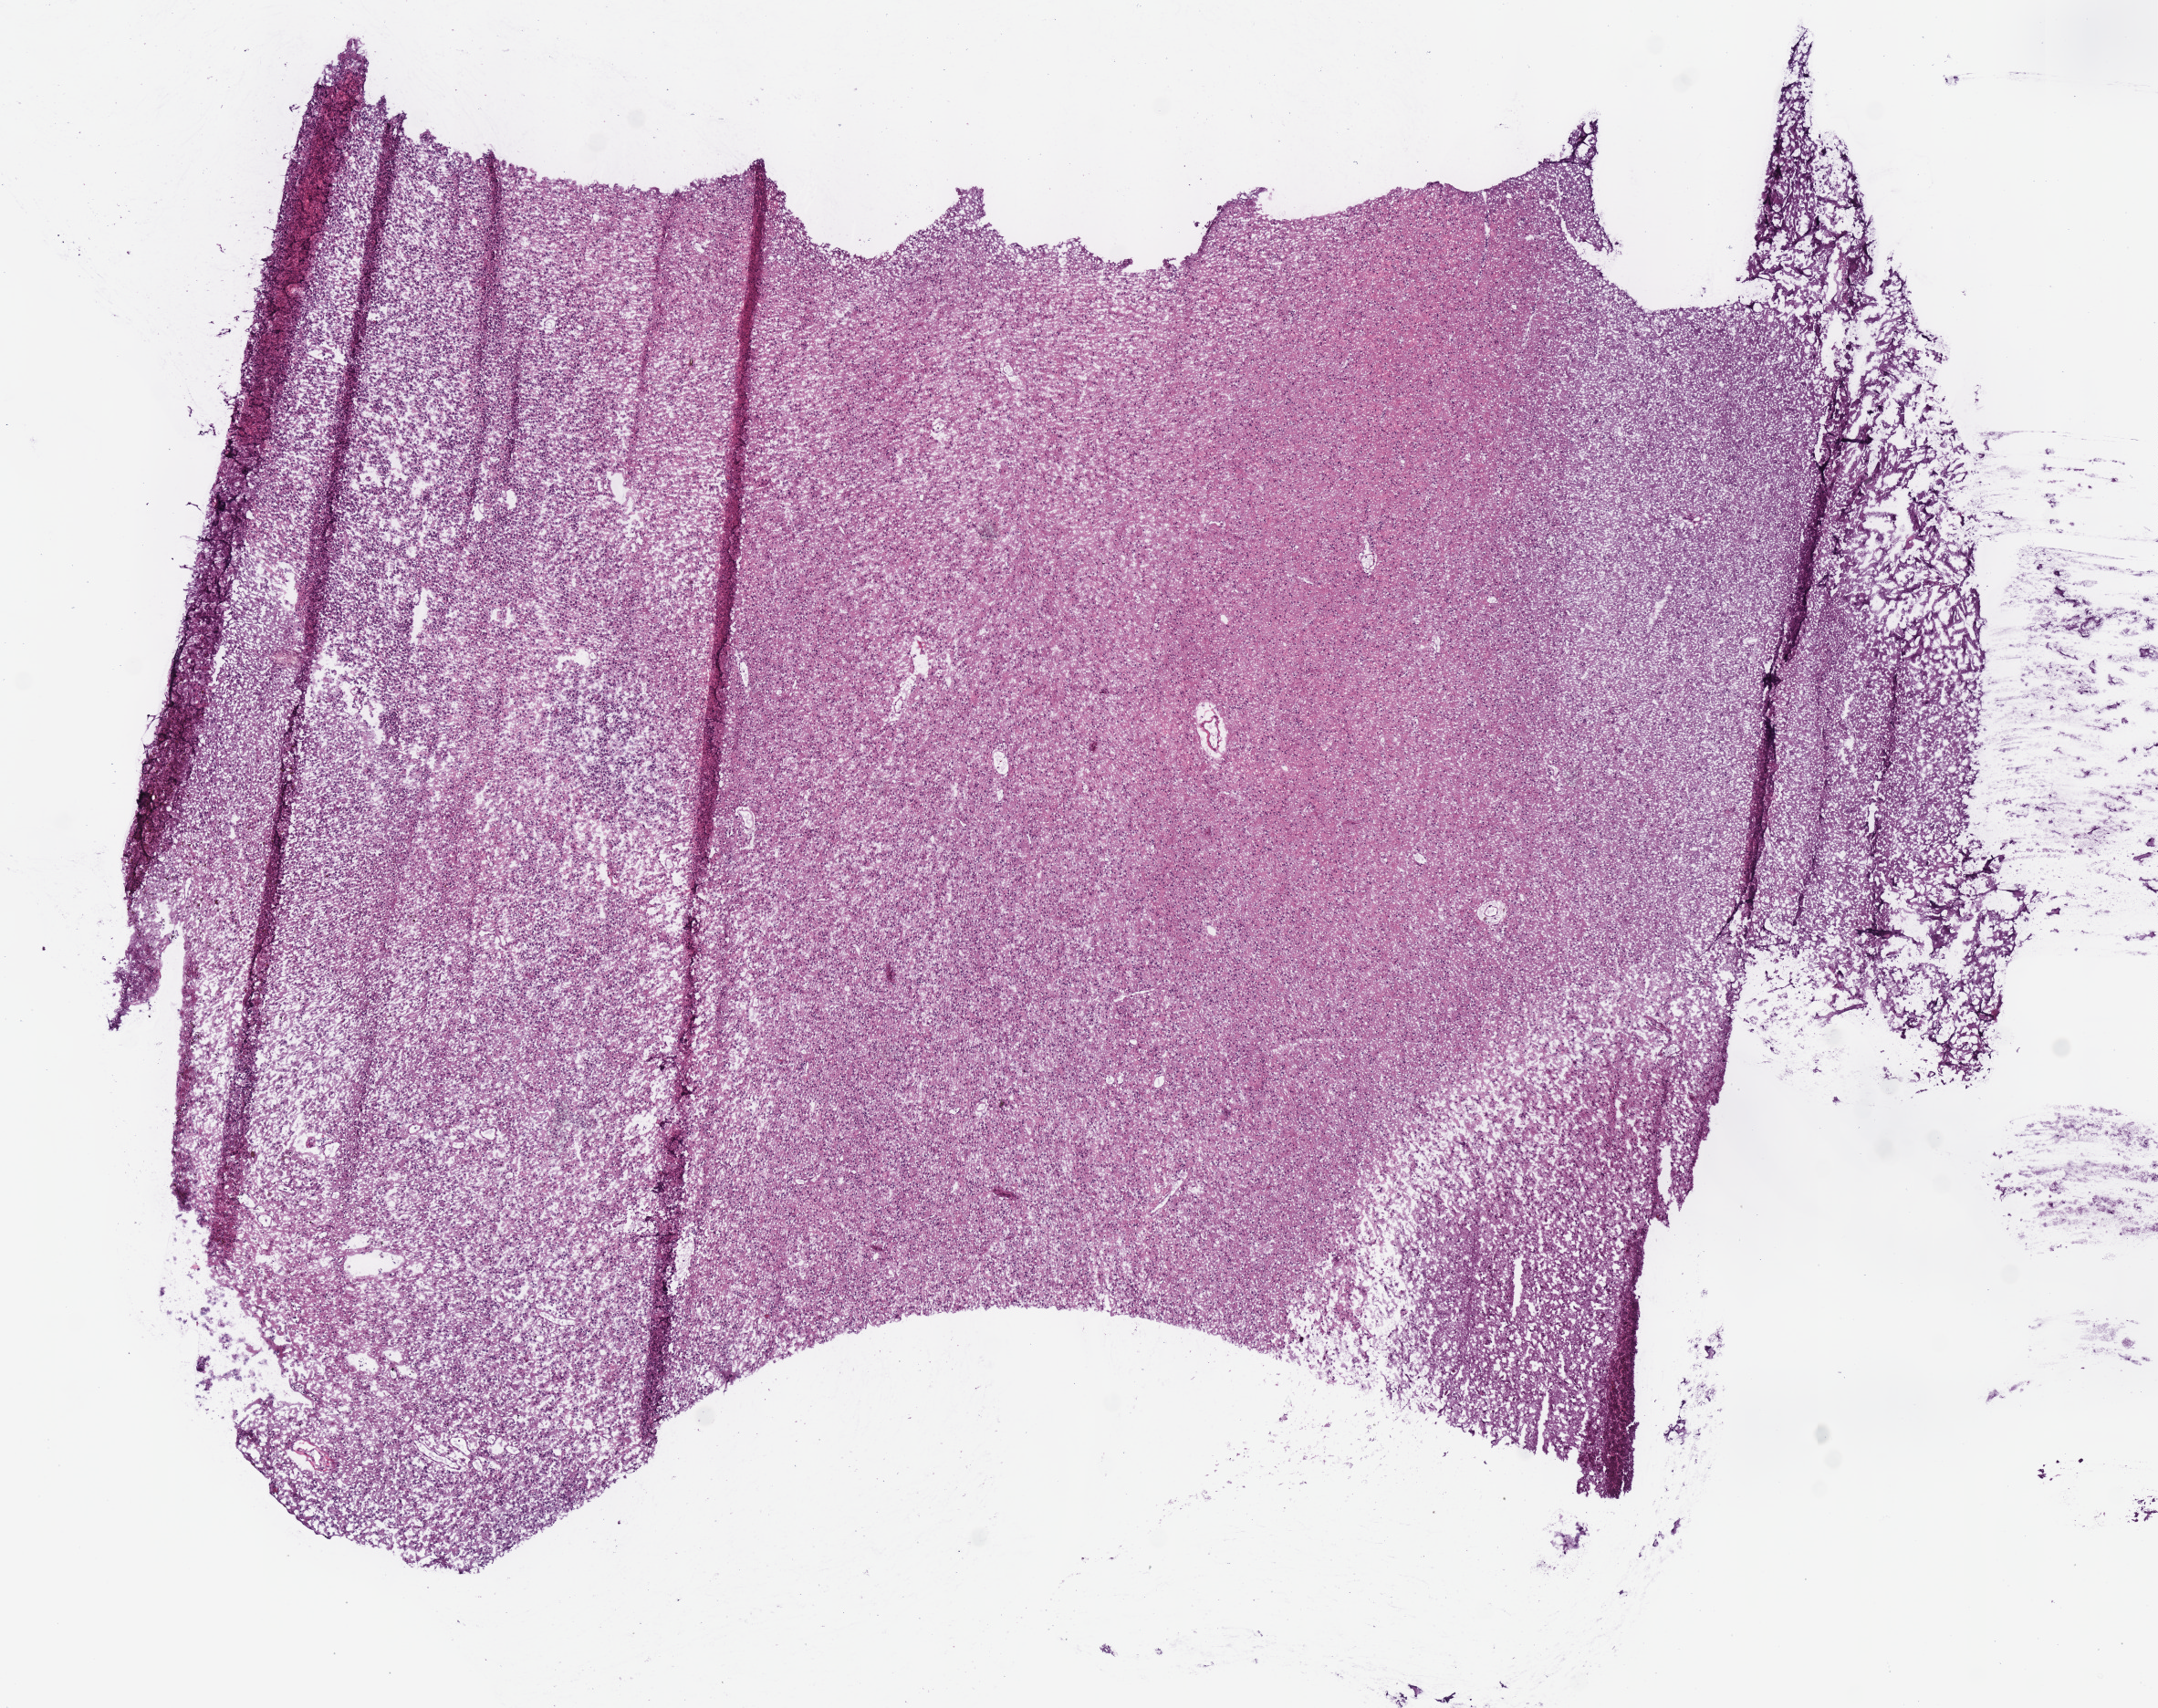
Digitized H&E tissue section (whole slide) — low-resolution overview of the scanned area, about 9.3 x 7.4 mm (slide scanned at 40x), frozen section from the bottom of the tissue portion, brain, primary tumour sample. Male, age 31 years at initial diagnosis. Histologic grade: G2 (moderately differentiated). Composition of this section per pathologist review: tumour cells 100%, tumour nuclei 75%, normal cells 0%, stromal cells 0%, necrosis 0%.
• diagnosis: Oligodendroglioma, NOS (cerebrum)